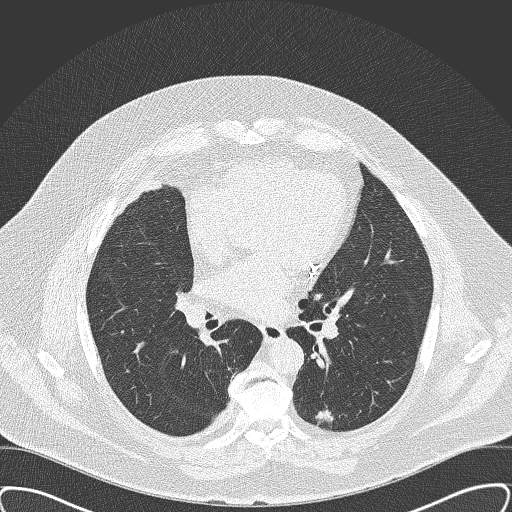
Low-dose screening chest CT, axial slice; third screening round (two years after baseline); lung window (W 1500 / L -600 HU); lung (sharp) reconstruction kernel (B50f); slice 89 of 161 in the series; 512 × 512 image matrix, field of view 400 × 400 mm. Male, age 63 years at enrolment.
• Expert reader's lesion annotation, bounding box (x1, y1, x2, y2) in pixels: (302, 391, 354, 437).
• The screening reader recorded 2 non-calcified nodules or masses ≥4 mm on this exam; which of them this box marks is not recorded.
• Official screen result: positive, other.
• Participant outcome: lung cancer diagnosed 47 days after this screen — squamous cell carcinoma, NOS, left lower lobe, moderately differentiated (G2), stage IA (AJCC 6th edition), 15 mm at pathology.